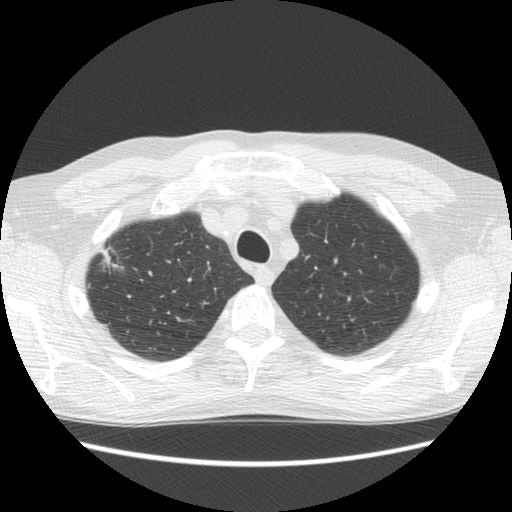
Low-dose screening chest CT, one axial slice. Slice 102 of 125 in the series (ordered by position). Reconstruction kernel STANDARD. 120 kVp. Lung window (W 1500 / L -600 HU). 2.5 mm slice thickness. 512 × 512 image matrix, field of view 350 × 350 mm.
Structures marked on this image (manually delineated by an expert):
- lesion 1 (tumor, upper lobe of right lung): bounding box <99,249,111,267> (left, top, right, bottom; pixels)